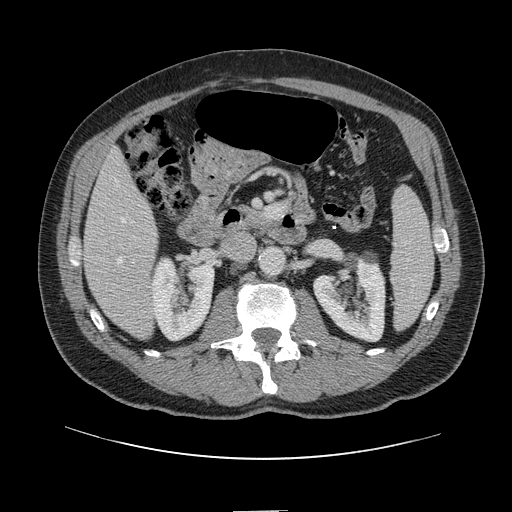
Contrast-enhanced abdominal CT, one axial slice. Position 43 of 161 along the scan axis. 120 kVp. Soft-tissue window (W 400 / L 40 HU). 512 × 512 image matrix. Male patient, age 66 years. Case-level facts recorded for this patient, not image findings: diagnosis: colorectal cancer liver metastases, imaged before liver resection; multiple liver metastases: no; largest metastasis: 3.5 cm.
Annotated regions visible in this slice (outlined manually by an expert reader):
- hepatic veins: bounding box [x1, y1, x2, y2] px = [118, 218, 125, 263]
- liver: [84, 153, 157, 339]
- planned liver remnant (the part of the liver to remain after resection): [84, 153, 154, 272]